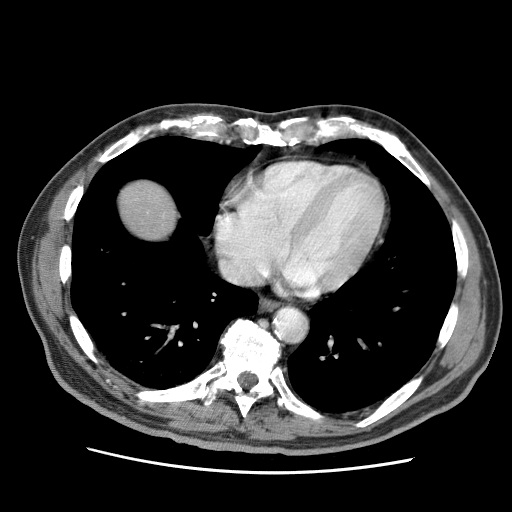
Contrast-enhanced abdominal CT (liver protocol), one axial slice. Position 67 of 75 along the scan axis. 120 kVp. Soft-tissue window (W 400 / L 40 HU). 2.5 mm slice thickness. 512 × 512 image matrix. Case-level facts recorded for this patient, not image findings: diagnosis: hepatocellular carcinoma (patient treated with transarterial chemoembolisation; whether this scan precedes or follows treatment is not stated here); TNM stage (as recorded): Stage-IIIA; Child-Pugh class: A; tumour differentiation: well differentiated.
Structures marked on this image (semi-automatic segmentation, software-assisted and operator-edited):
- liver parenchyma outside the tumour (the mass and vessels are separate outlines, so this box may not span the whole liver): bounding box (x1, y1, x2, y2) in pixels: (118, 180, 177, 240)